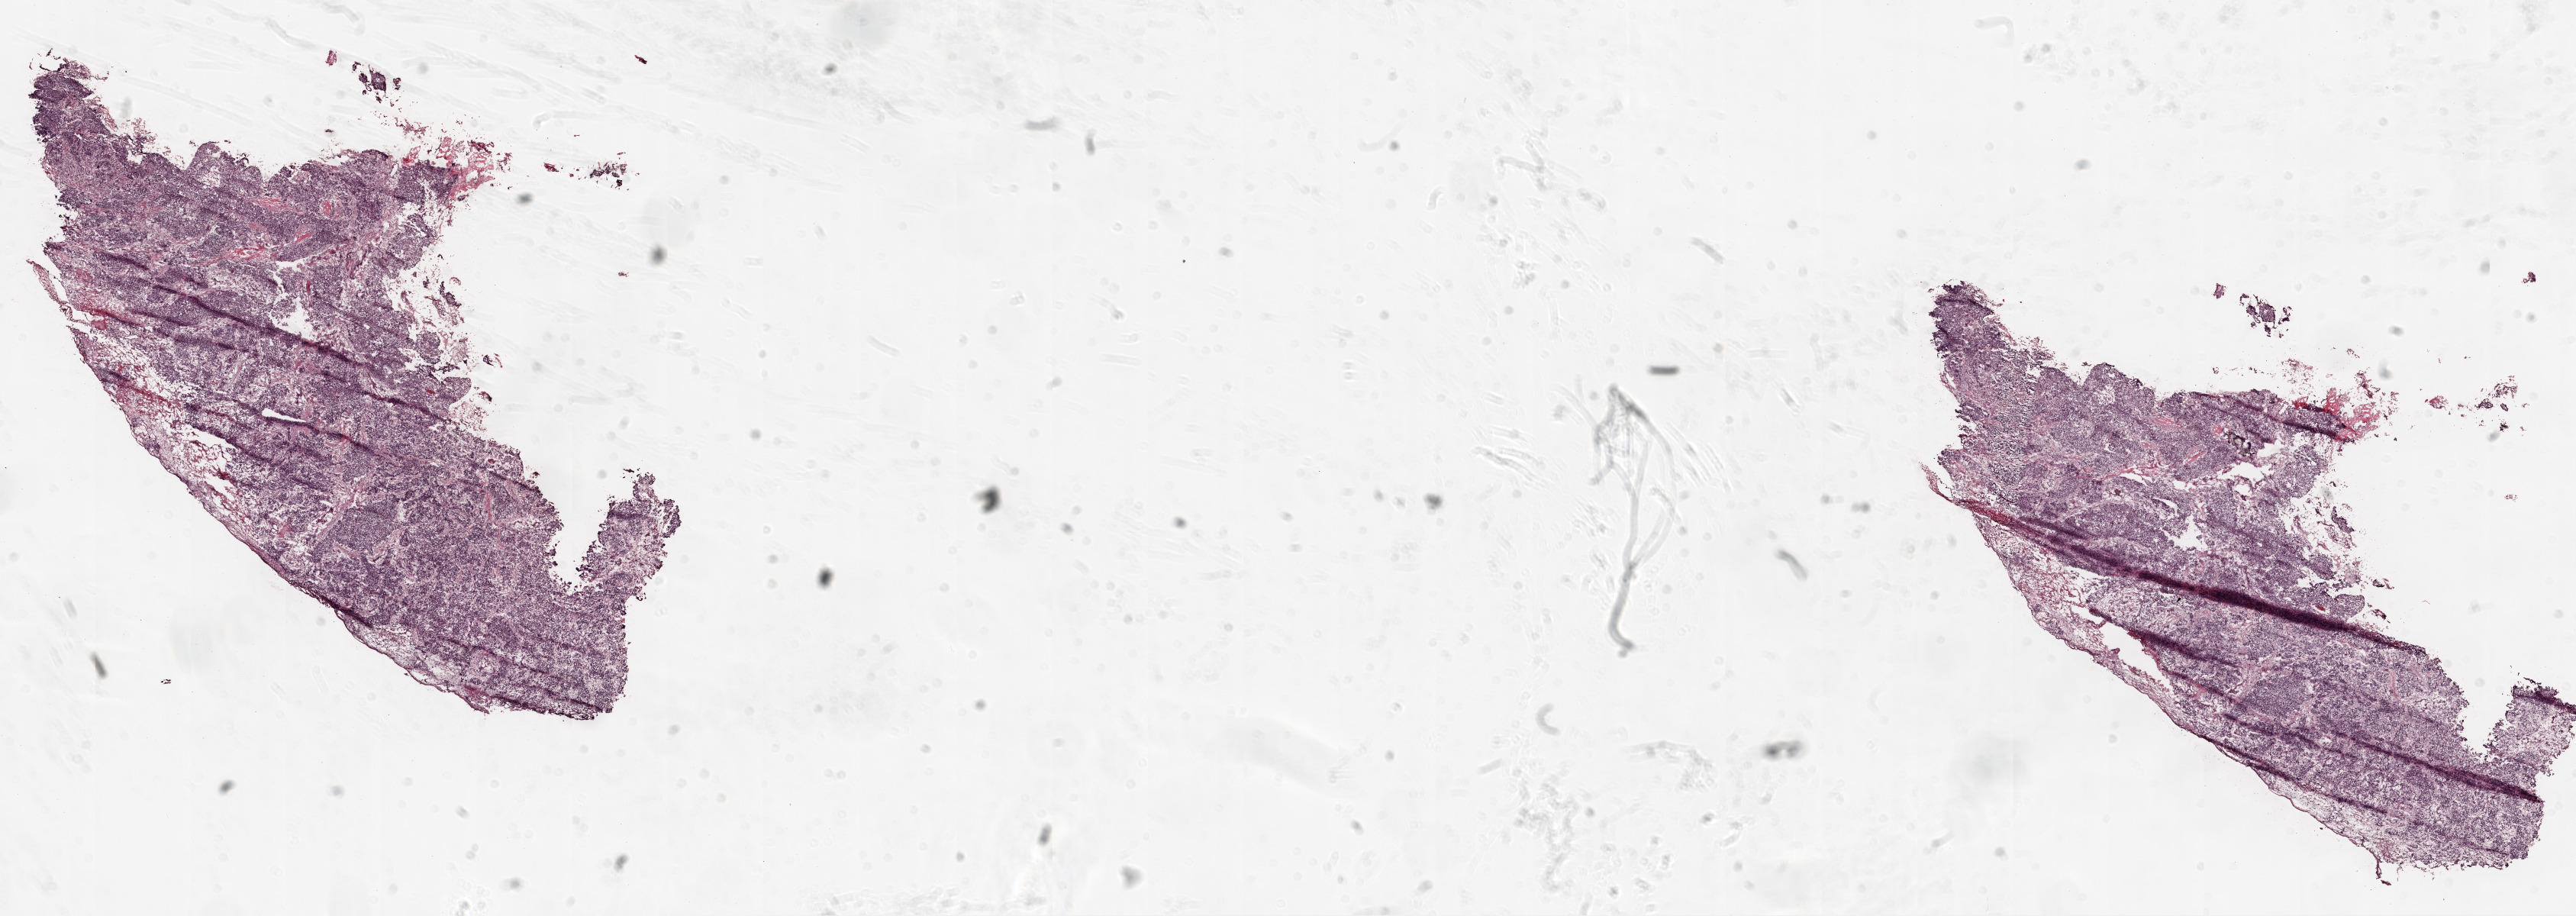
Whole-slide histology image, H&E-stained, low-resolution overview of the scanned area, about 27.1 x 9.6 mm, frozen section from the top of the tissue portion, sample: primary tumour, ovary. Female patient; age at initial diagnosis 47 years. Histologic grade: G2 (moderately differentiated). Composition of this section per pathologist review: tumour cells 80%, tumour nuclei 85%, normal cells 0%, stromal cells 20%, necrosis 0%. Inflammatory infiltration, as recorded: lymphocyte infiltration 5%.
FIGO stage: IIIC. Laterality: bilateral. Diagnosis: Serous cystadenocarcinoma, NOS.